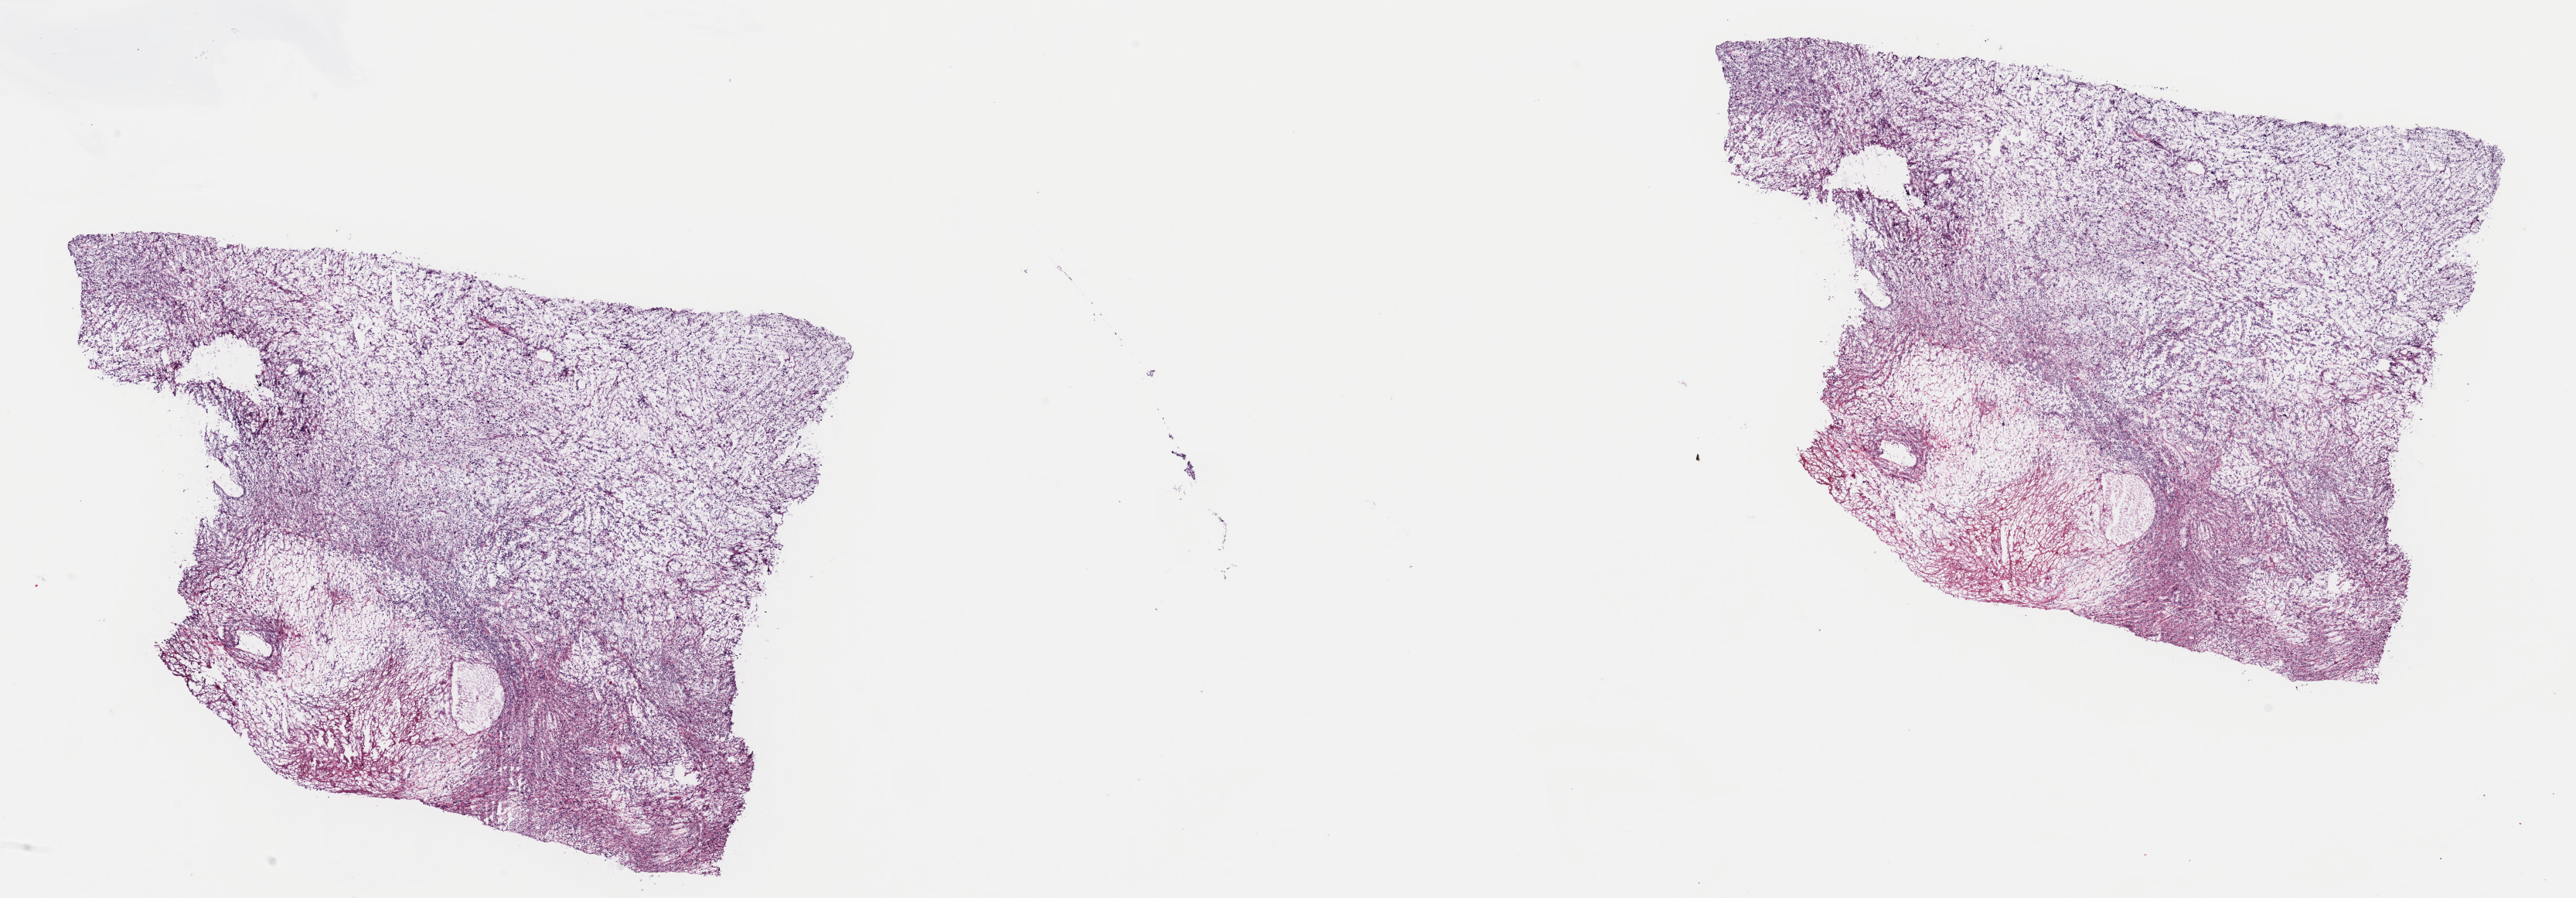
Whole-slide histology image, Hematoxylin and eosin (H&E) stained — shown as a low-resolution overview of the whole scanned area (about 26.3 x 9.2 mm, slide scanned at 40x), frozen section from the top of the tissue portion, connective, subcutaneous and other soft tissues, primary tumour sample. Patient: female, age at initial diagnosis 50 years. Slide review estimates, as recorded: tumour cells 70%, tumour nuclei 80%, normal cells 0%, stromal cells 20%, necrosis 10%. Inflammatory infiltration, as recorded: lymphocyte infiltration 5%, monocyte infiltration 5%, neutrophil infiltration 0%.
Diagnosis: Fibromyxosarcoma (connective, subcutaneous and other soft tissues of thorax).